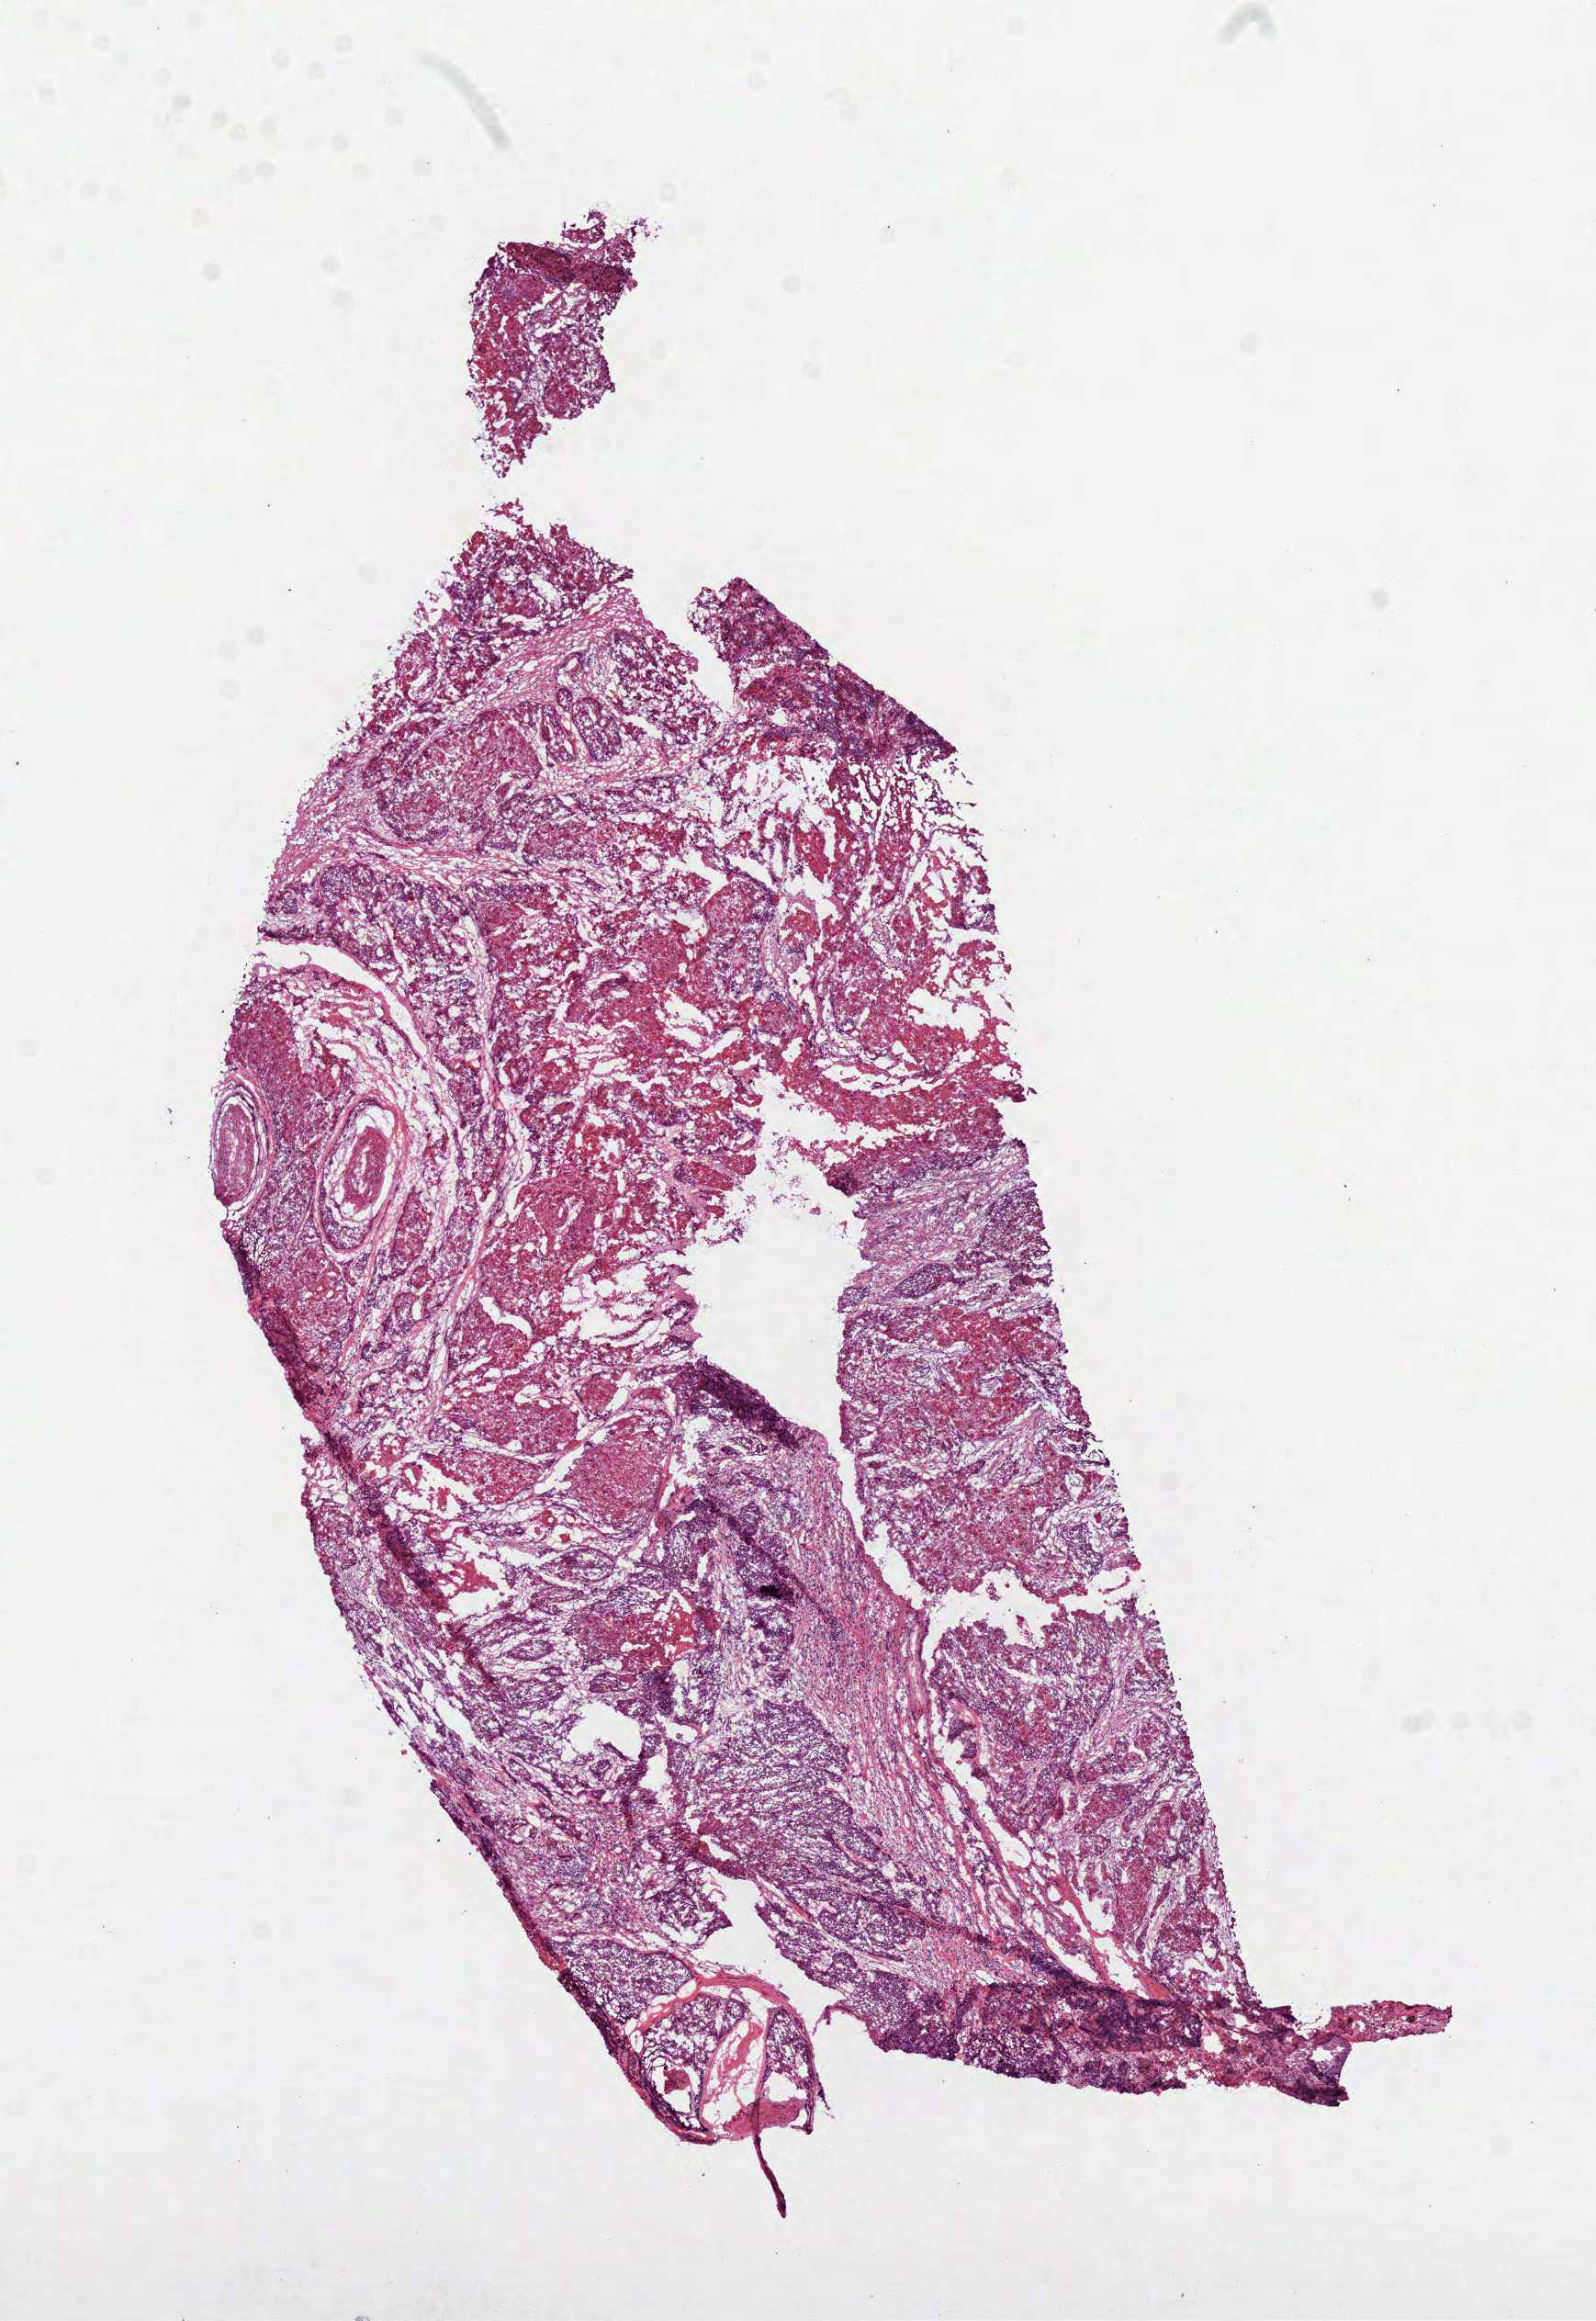
Digitized Hematoxylin and eosin (H&E) stained tissue section (whole slide) — whole scanned area (about 7.0 x 10.2 mm, acquisition: 40x scan) shown as a low-resolution overview; frozen section from the top of the tissue portion; head and neck, primary tumour sample. Male, age 67 years at initial diagnosis. Histologic grade: G3 (poorly differentiated). Composition of this section per pathologist review: tumour cells 80%, tumour nuclei 80%, normal cells 0%, stromal cells 0%, necrosis 20%. Infiltration values recorded for this section: lymphocyte infiltration 4%, monocyte infiltration 0%, neutrophil infiltration 0%.
Pathologic diagnosis: Squamous cell carcinoma, NOS (larynx, NOS). AJCC pathologic stage: IVA (7th edition).